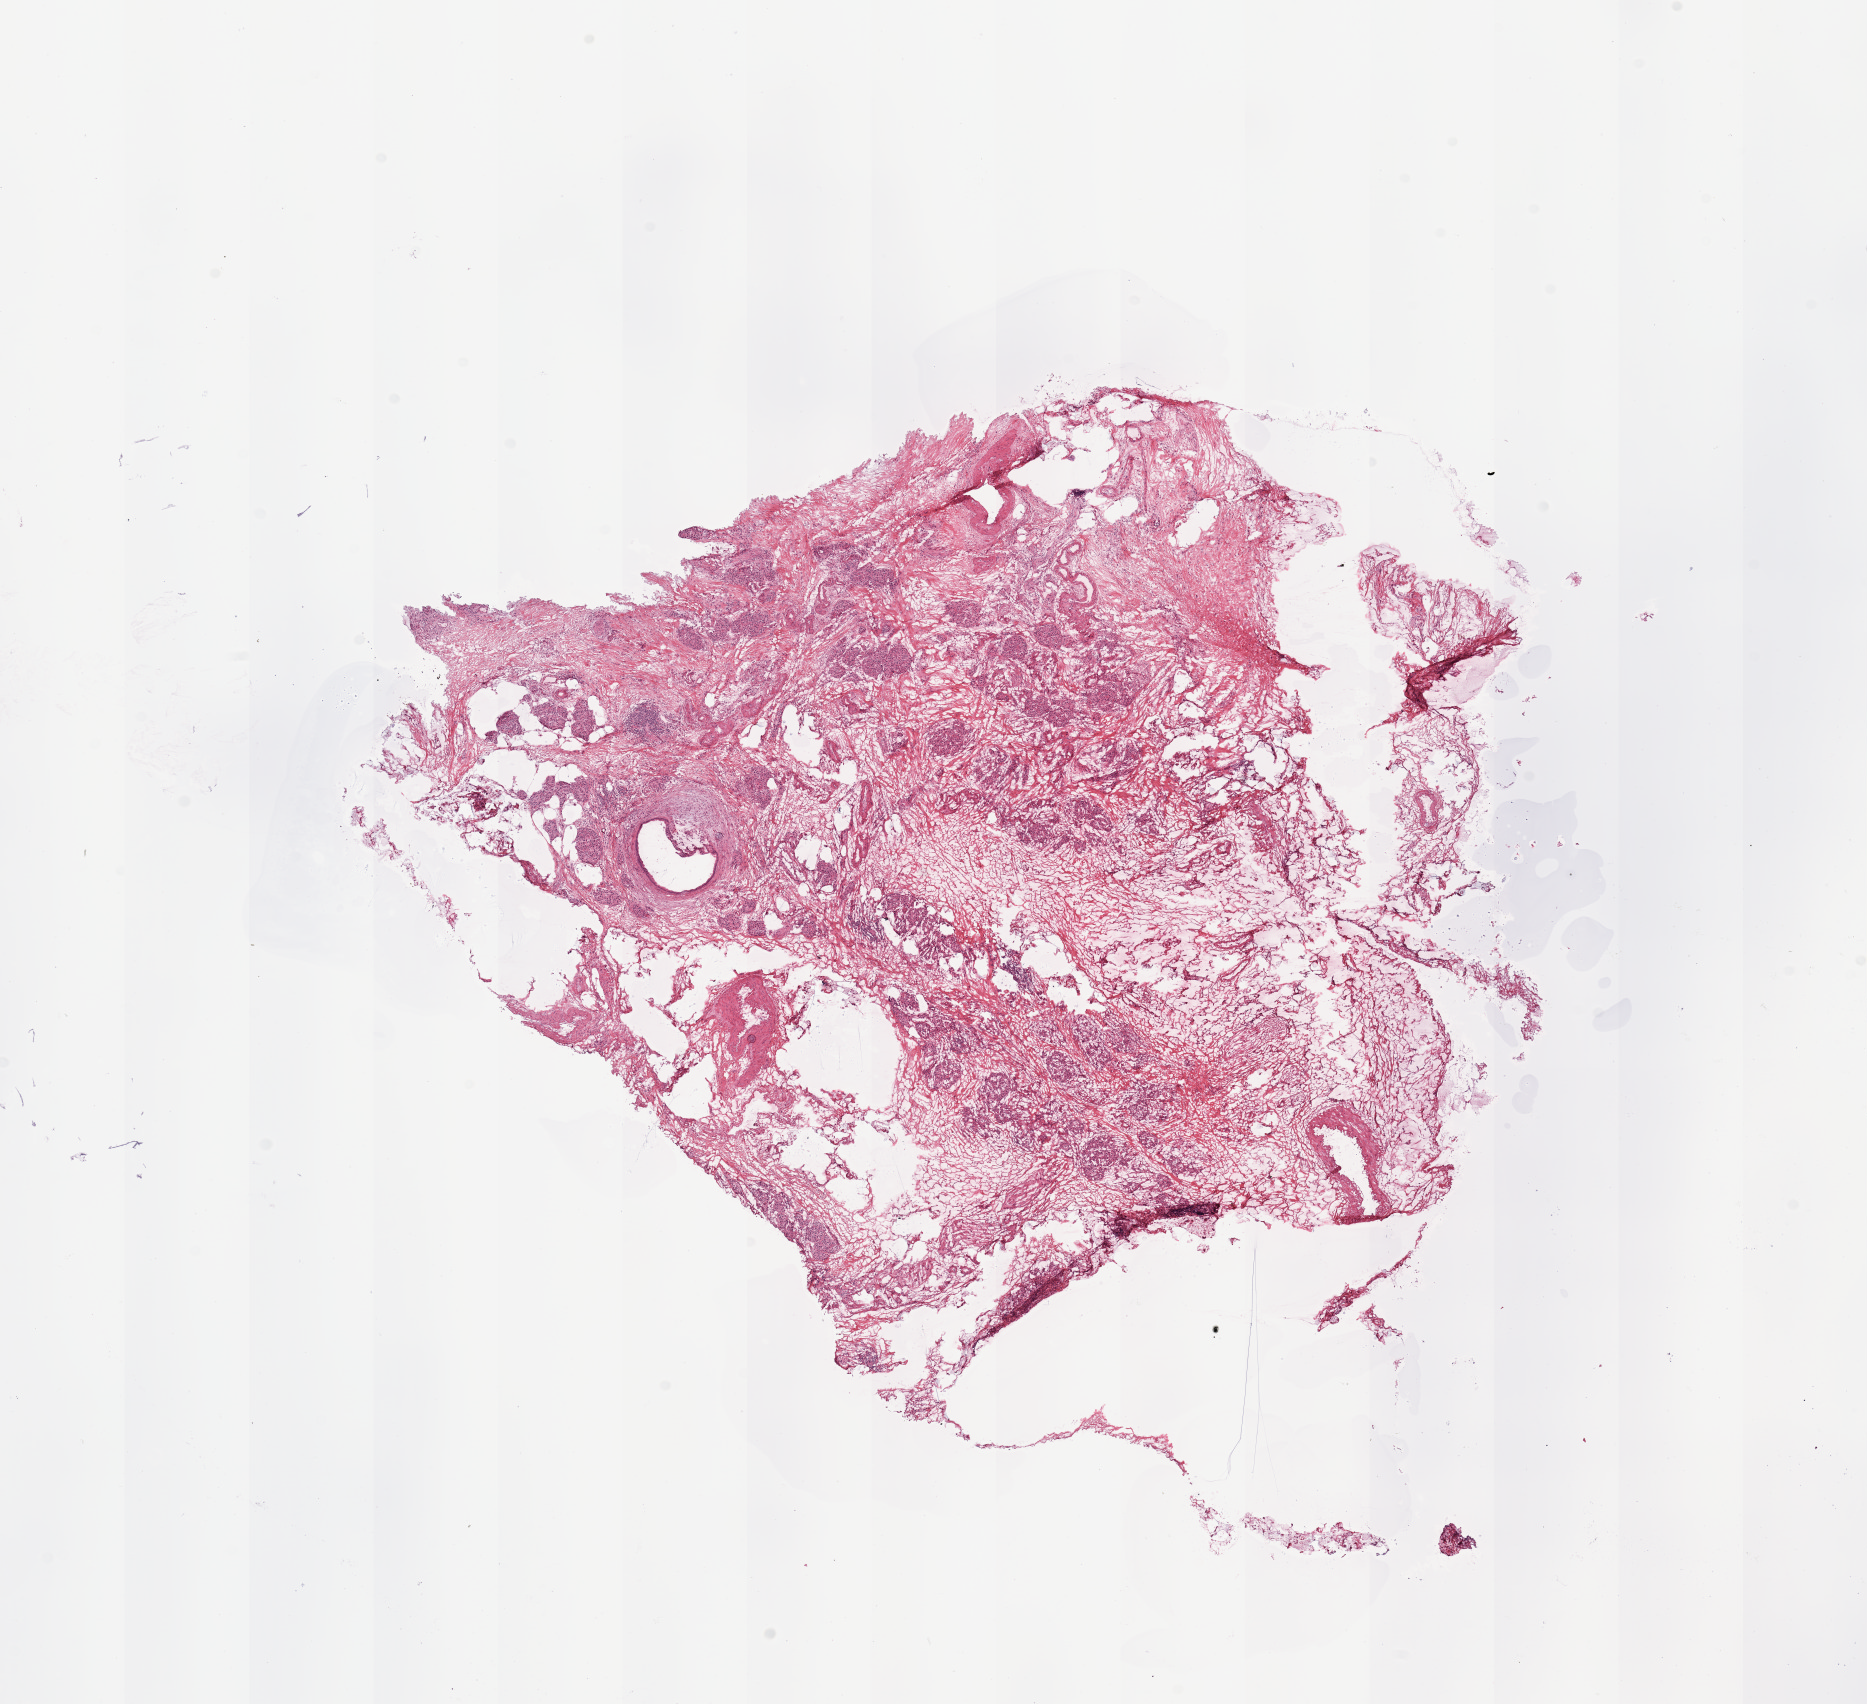
Whole-slide histology image, H&E-stained — whole scanned area (about 14.8 x 13.5 mm, from a 20x scan) shown as a low-resolution overview, pancreas, normal (non-tumour) tissue. 62-year-old female patient.
This section: normal (non-tumour) tissue from the same patient. Patient diagnosis: Infiltrating duct carcinoma, NOS.